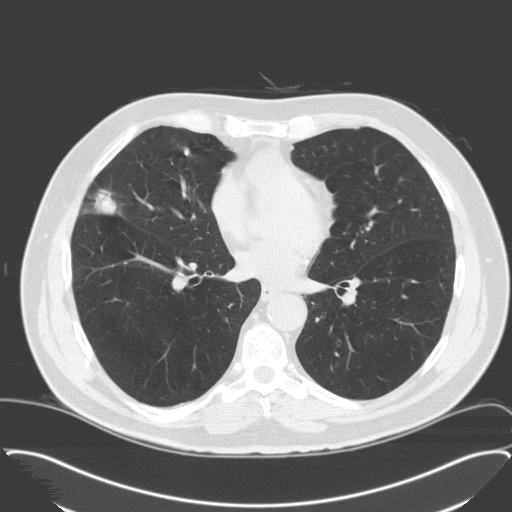
Low-dose screening chest CT, one axial slice; position 84 of 174 along the scan axis; lung window (W 1500 / L -600 HU); 3.2 mm slice thickness; 512 × 512 image matrix, field of view 400 × 400 mm.
Structures marked on this image (expert manual segmentation):
- lesion 1 (tumor, middle lobe of right lung): bounding box [x1, y1, x2, y2] px = [93, 189, 117, 214]